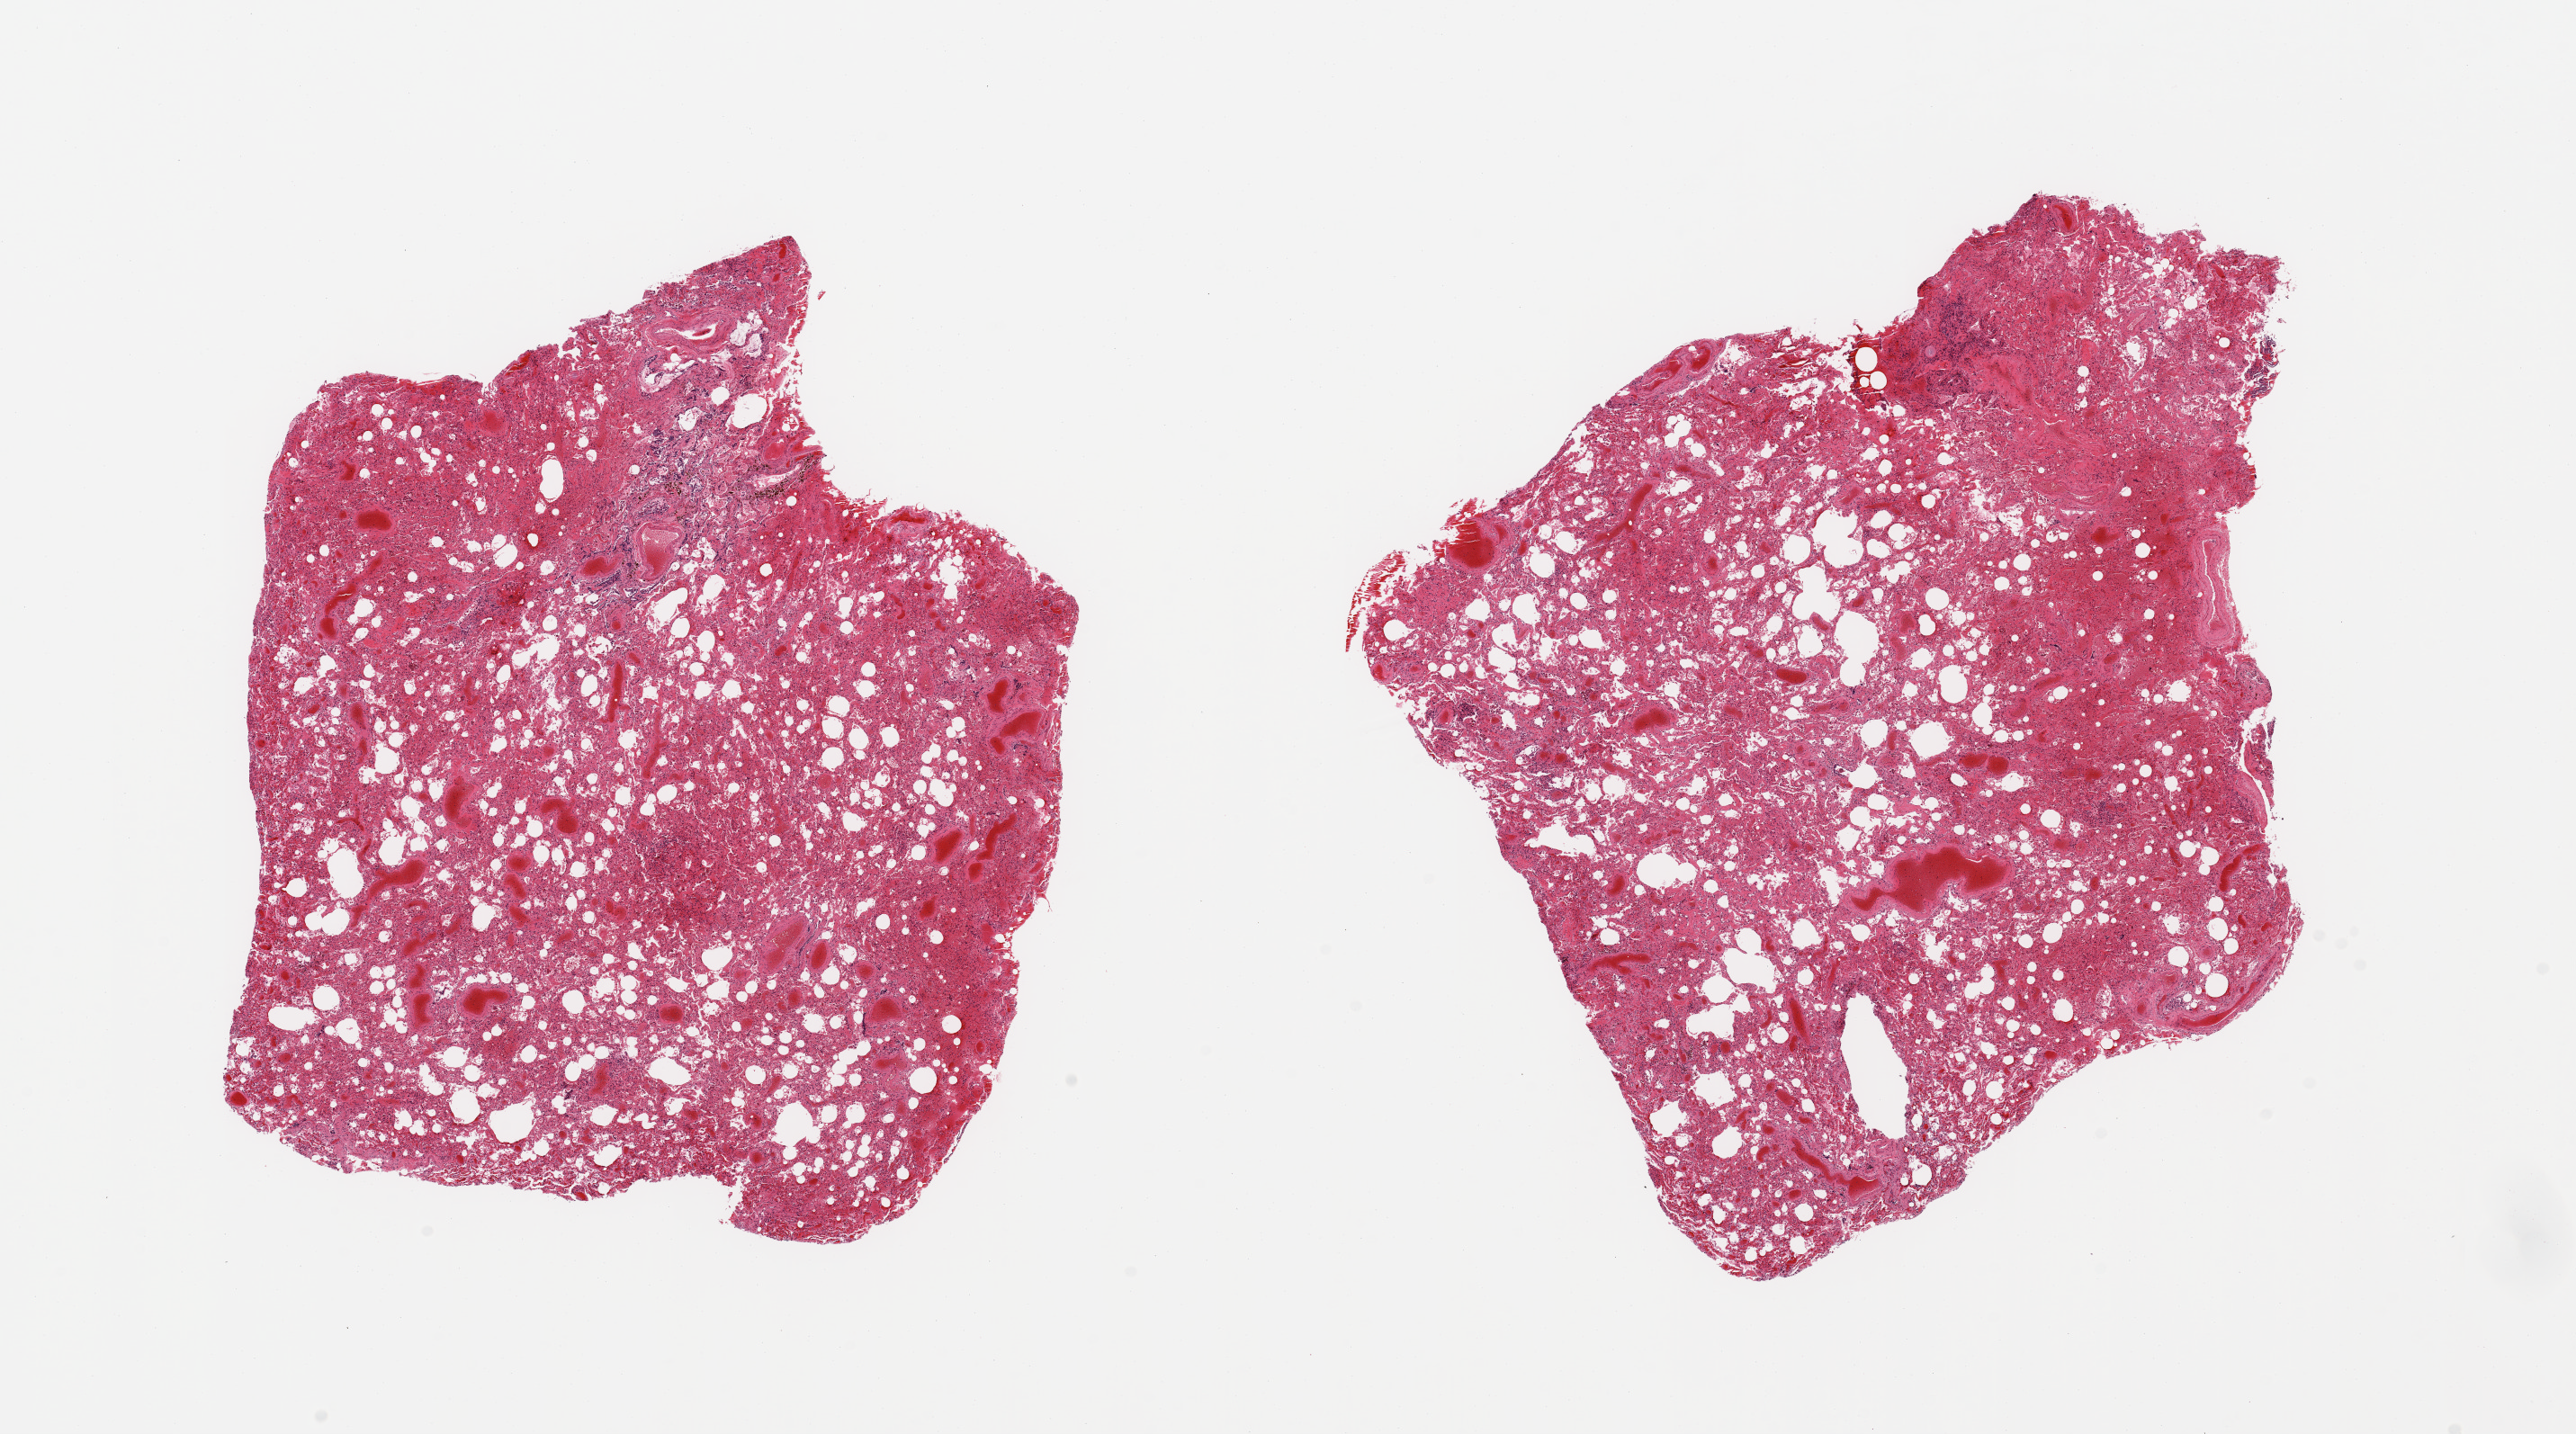
Whole-slide image, H&E stain, brightfield, low-resolution overview of the scanned area, about 22.6 x 12.6 mm, PAXgene-fixed, paraffin-embedded tissue, sampled site (target tissue): lung, donor tissue sample. Female donor.
* reviewer comment on this tissue sample: 2 pieces, moderate/marked congestions/edema/ diffuse alveolar damage